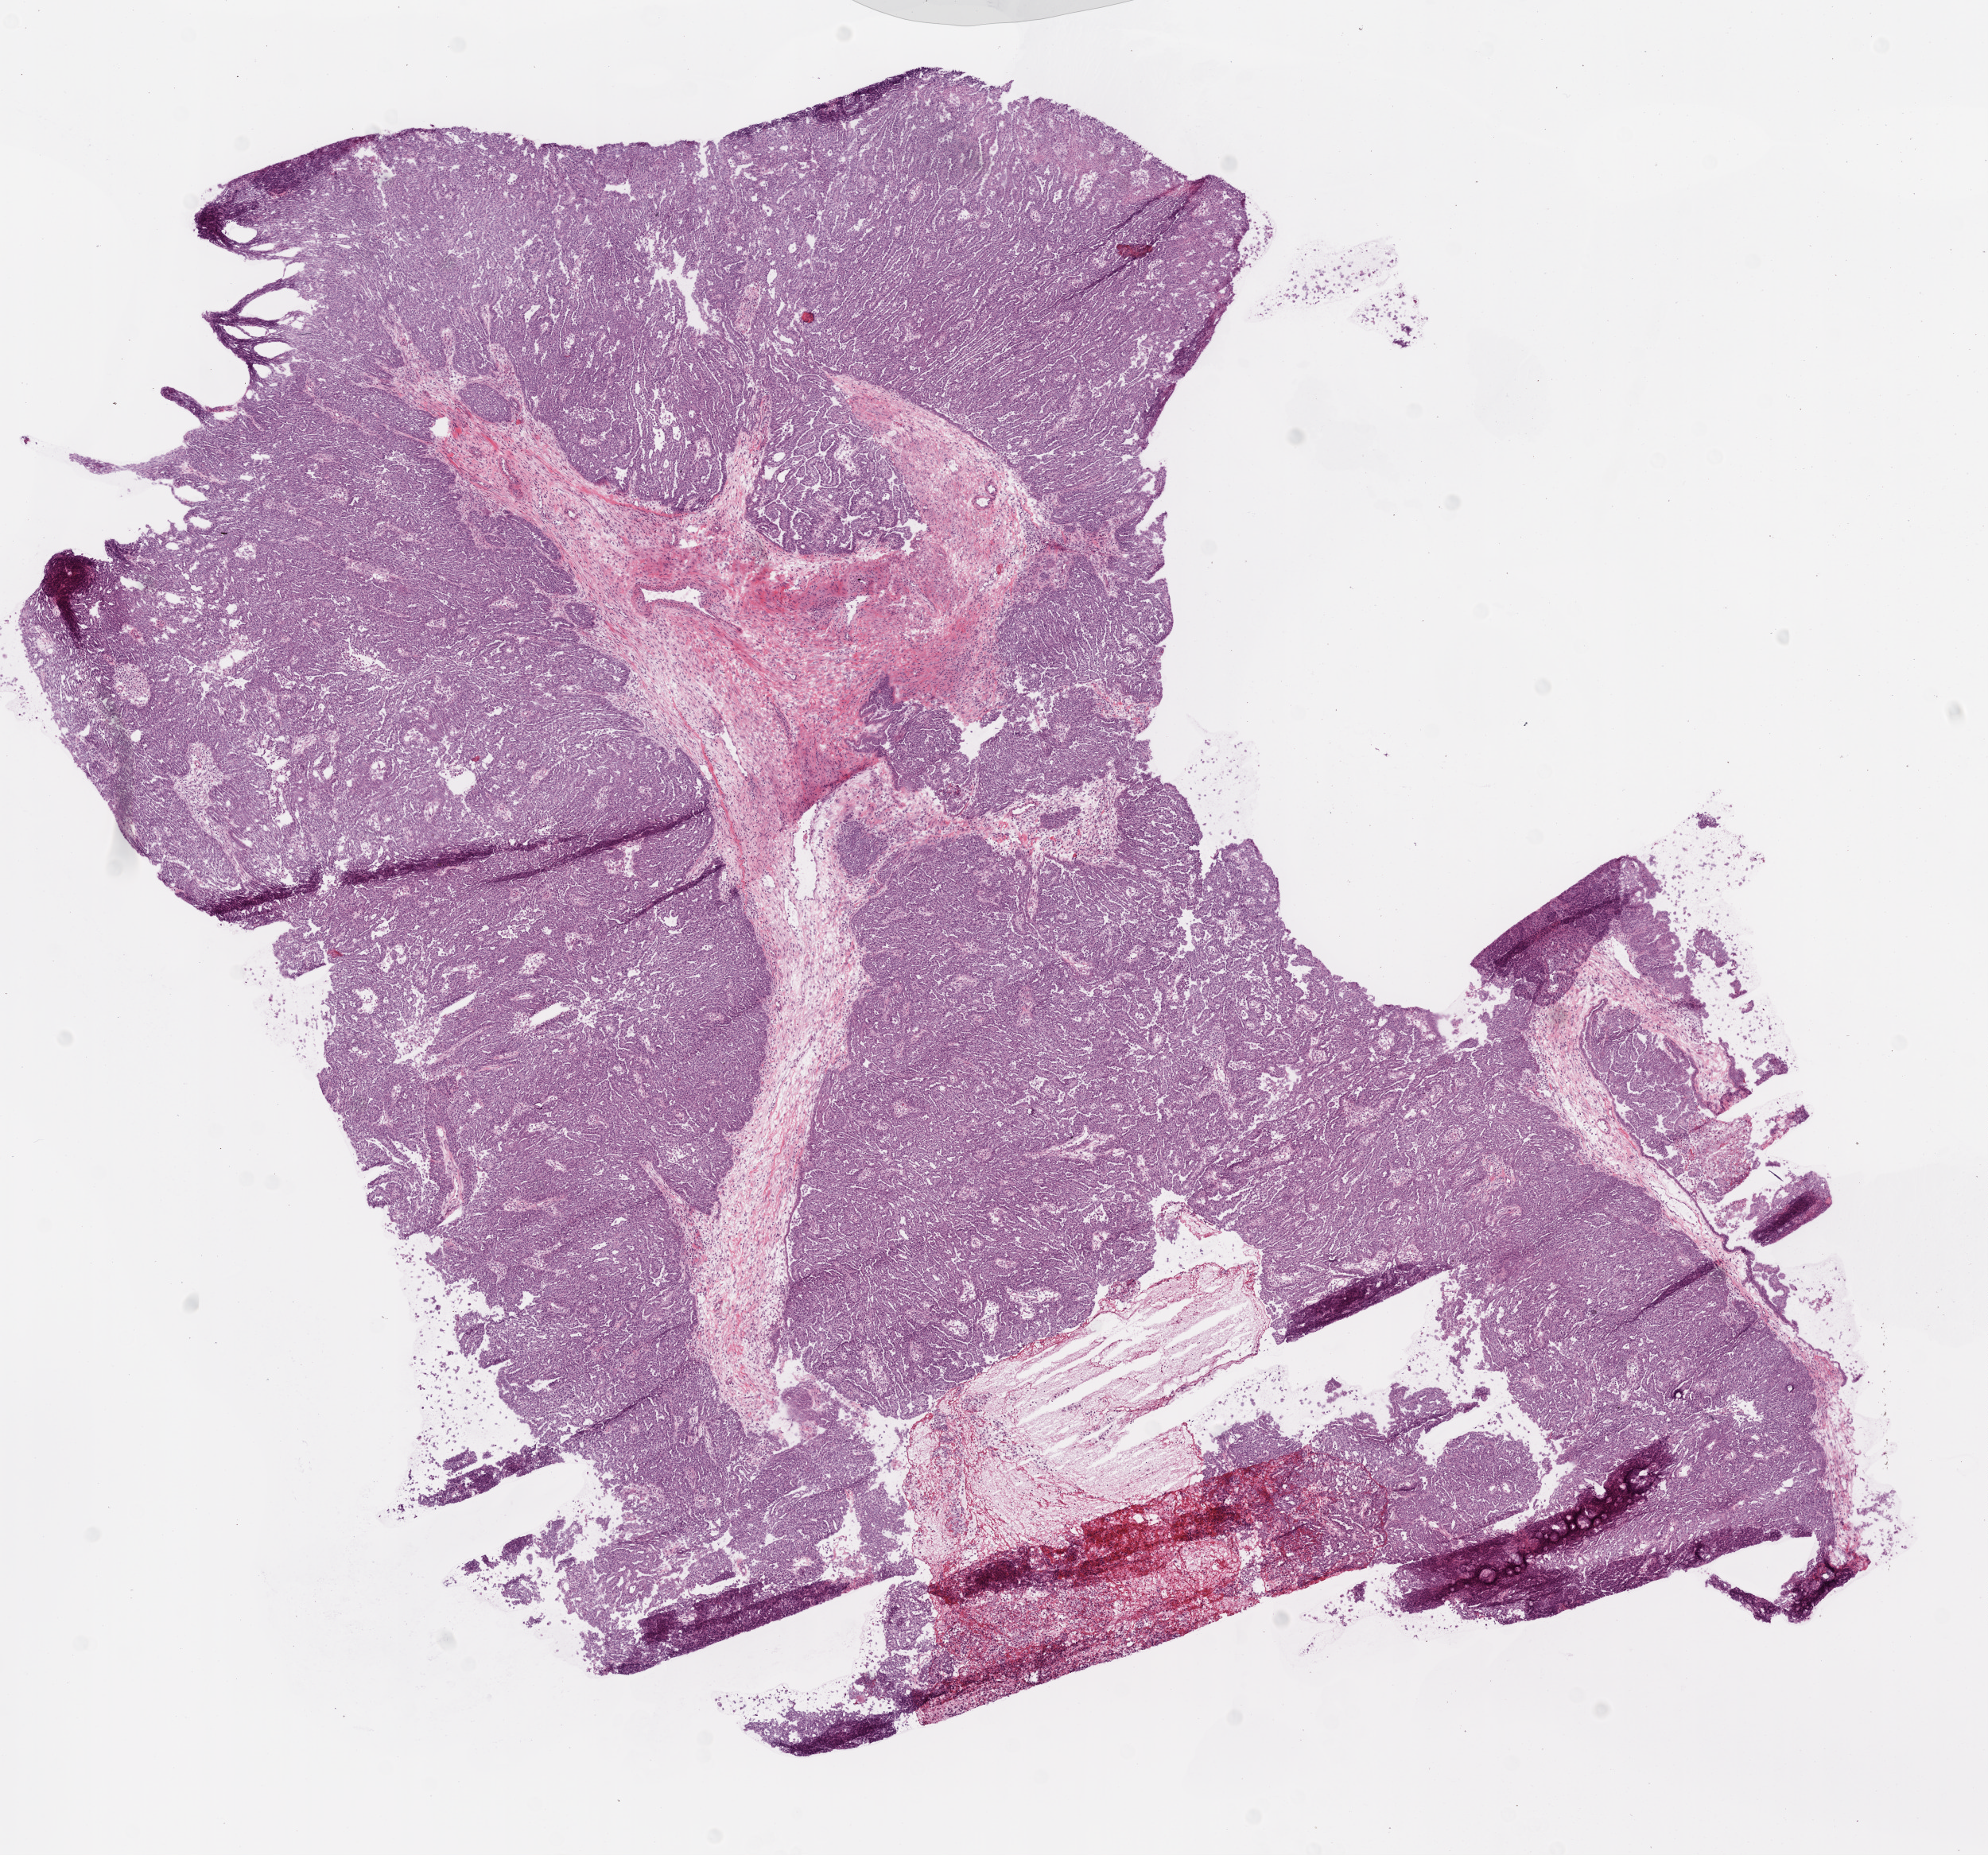
Hematoxylin and eosin (H&E) stained whole-slide image, shown as a low-resolution overview of the whole scanned area (about 10.0 x 9.4 mm). Frozen section from the top of the tissue portion. Ovary, primary tumour sample. Female, age 58 years at initial diagnosis. Histologic grade: G3 (poorly differentiated). Slide review estimates, as recorded: tumour cells 87%, tumour nuclei 85%, normal cells 8%, stromal cells 0%, necrosis 5%.
Histologic diagnosis: Serous cystadenocarcinoma, NOS. Laterality: left. FIGO stage: IV.